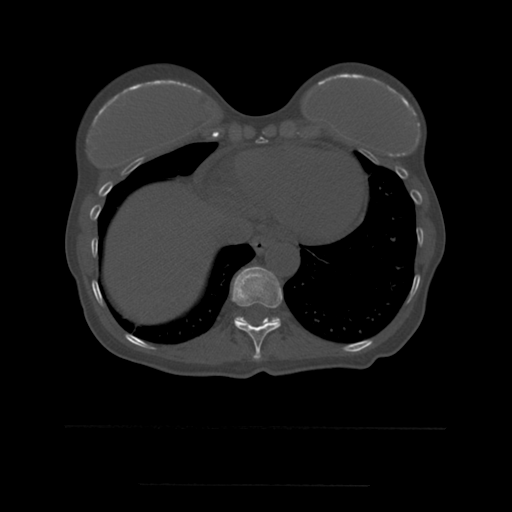
CT including the spine, one axial slice; position 296 of 544 along the scan axis; bone window (W 1800 / L 400 HU); 1.25 mm slice thickness; 512 × 512 image matrix, field of view 350 × 350 mm. Patient age 58 years. Case-level facts recorded for this patient, not image findings: primary cancer: lung.
Annotated regions visible in this slice (semi-automatically segmented with operator editing):
- T10 vertebra: bounding box [x1, y1, x2, y2] px = [232, 267, 283, 360]
- T11 vertebra: [235, 317, 281, 323]